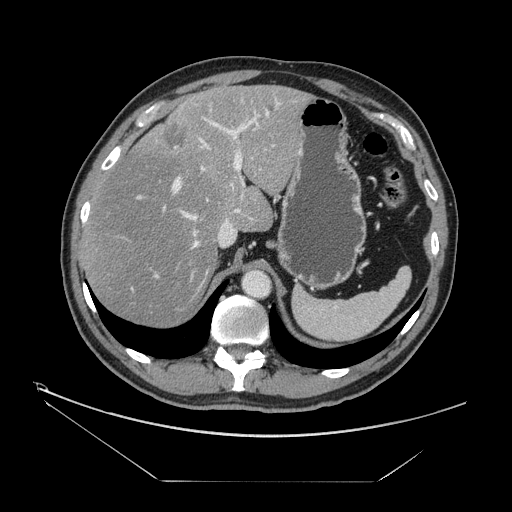
Contrast-enhanced abdominal CT, one axial slice. Reconstruction kernel STANDARD. 120 kVp. Soft-tissue window (W 400 / L 40 HU). 2.5 mm slice thickness. 512 × 512 image matrix, field of view 440 × 440 mm. Male patient, age 65 years. From the clinical record (not read from this slice): diagnosis: colorectal cancer liver metastases, imaged before liver resection; multiple liver metastases: yes; largest metastasis: 4.2 cm; chemotherapy before resection: yes.
Annotated regions visible in this slice (expert manual segmentation):
- hepatic veins: bounding box <185,113,268,249> (left, top, right, bottom; pixels)
- liver: <83,85,307,328>
- planned liver remnant (the part of the liver to remain after resection): <84,86,307,328>
- portal vein (with intrahepatic branches): <136,98,282,277>
- liver metastasis: <164,125,189,151>